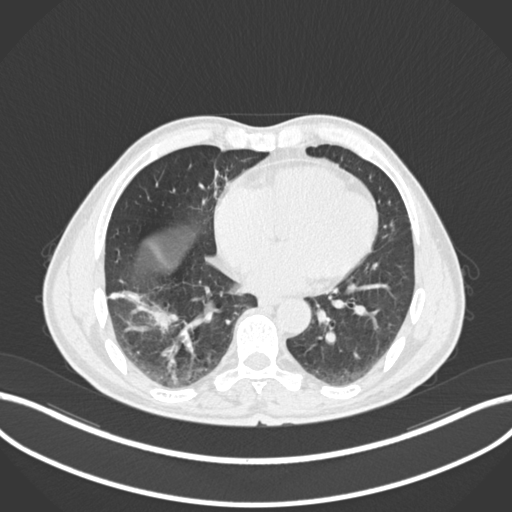
Chest CT, one axial slice; reconstruction kernel B30f; 120 kVp; lung window (W 1500 / L -600 HU); 1 mm slice thickness; 512 × 512 image matrix, field of view 400 × 400 mm. Male patient, age 58 years. Case-level facts recorded for this patient, not image findings: clinical TNM (as recorded): T3 N0 M0; histopathological grade: G2.
Outlined on this slice (bounding box drawn by a radiologist):
- lung tumour (recorded histology: squamous cell carcinoma): bounding box (x1, y1, x2, y2) in pixels: (108, 287, 177, 334)